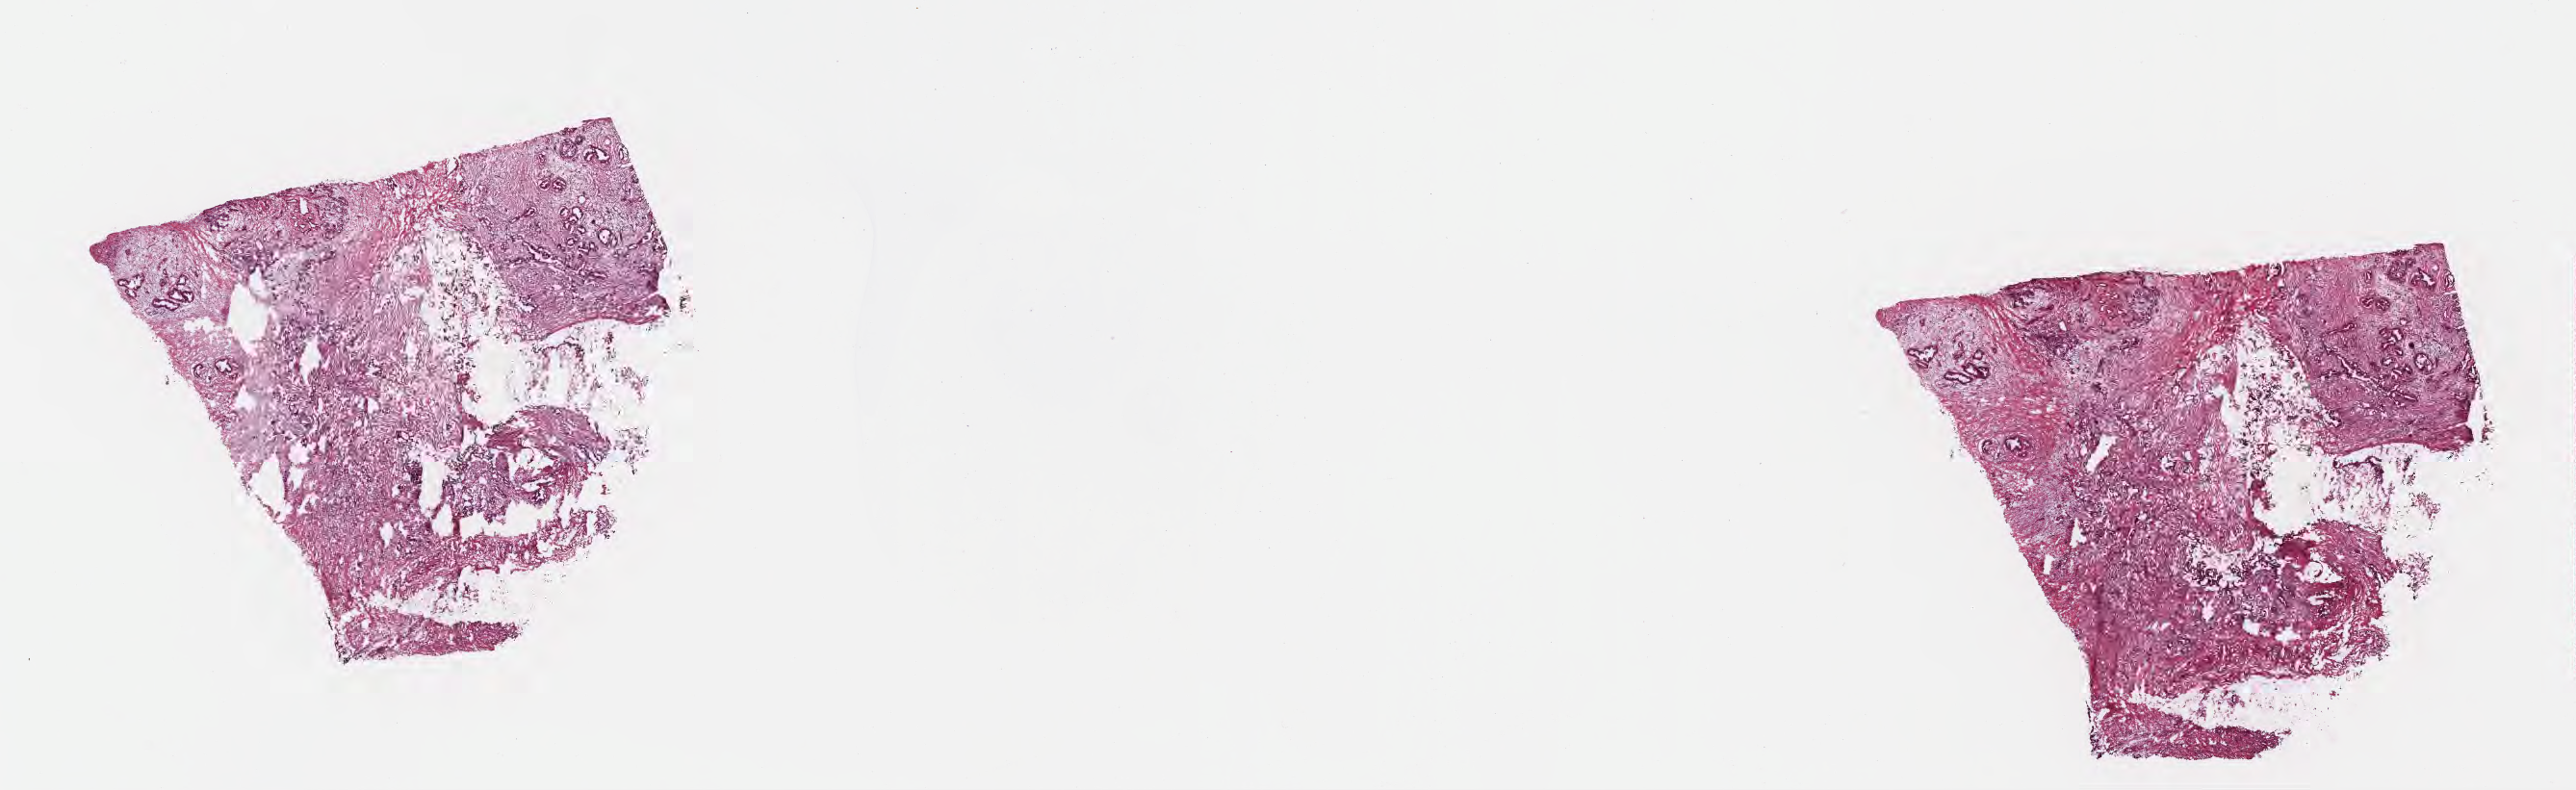
H&E whole-slide image, low-resolution overview of the scanned area, about 21.6 x 6.6 mm; frozen section (tissue freezing medium); primary tumor; anatomic site: head of pancreas. Male patient; age at initial diagnosis 74 years. Tumor grade: G3 (poorly differentiated). Pathologist review of this section (percent, as recorded): tumor cells 20%, tumor nuclei 55%, stromal cells 78%, necrosis 2%, normal cells 0%. Inflammatory infiltration, as recorded: lymphocyte infiltration 38%, monocyte infiltration 2%, neutrophil infiltration 0%.
Section: top of the tissue portion. Histologic diagnosis: Infiltrating duct carcinoma, NOS. AJCC pathologic stage: Stage IIB.